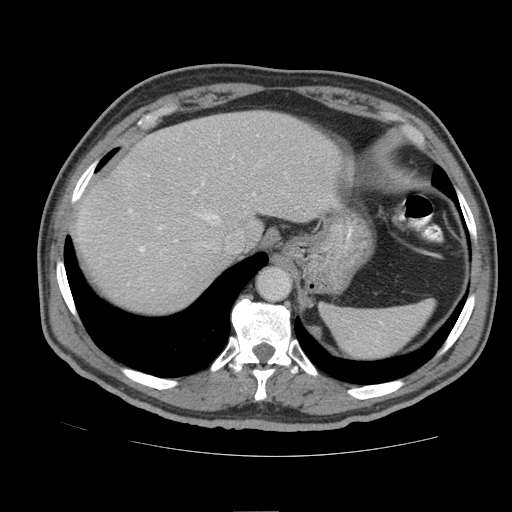
Contrast-enhanced abdominal CT (liver protocol), one axial slice; slice 69 of 105 in the series (ordered by position); reconstruction kernel STANDARD; soft-tissue window (W 400 / L 40 HU); 512 × 512 image matrix, field of view 380 × 380 mm. From the clinical record (not read from this slice): diagnosis: hepatocellular carcinoma (patient treated with transarterial chemoembolisation; whether this scan precedes or follows treatment is not stated here); TNM stage (as recorded): Stage-IIIB; Child-Pugh class: A; tumour nodularity: multinodular.
Annotated regions visible in this slice (semi-automatic segmentation, software-assisted and operator-edited):
- abdominal aorta: bounding box (x1, y1, x2, y2) in pixels: (259, 269, 289, 298)
- liver parenchyma outside the tumour (the mass and vessels are separate outlines, so this box may not span the whole liver): (74, 110, 342, 312)
- liver vessels: (129, 182, 255, 252)